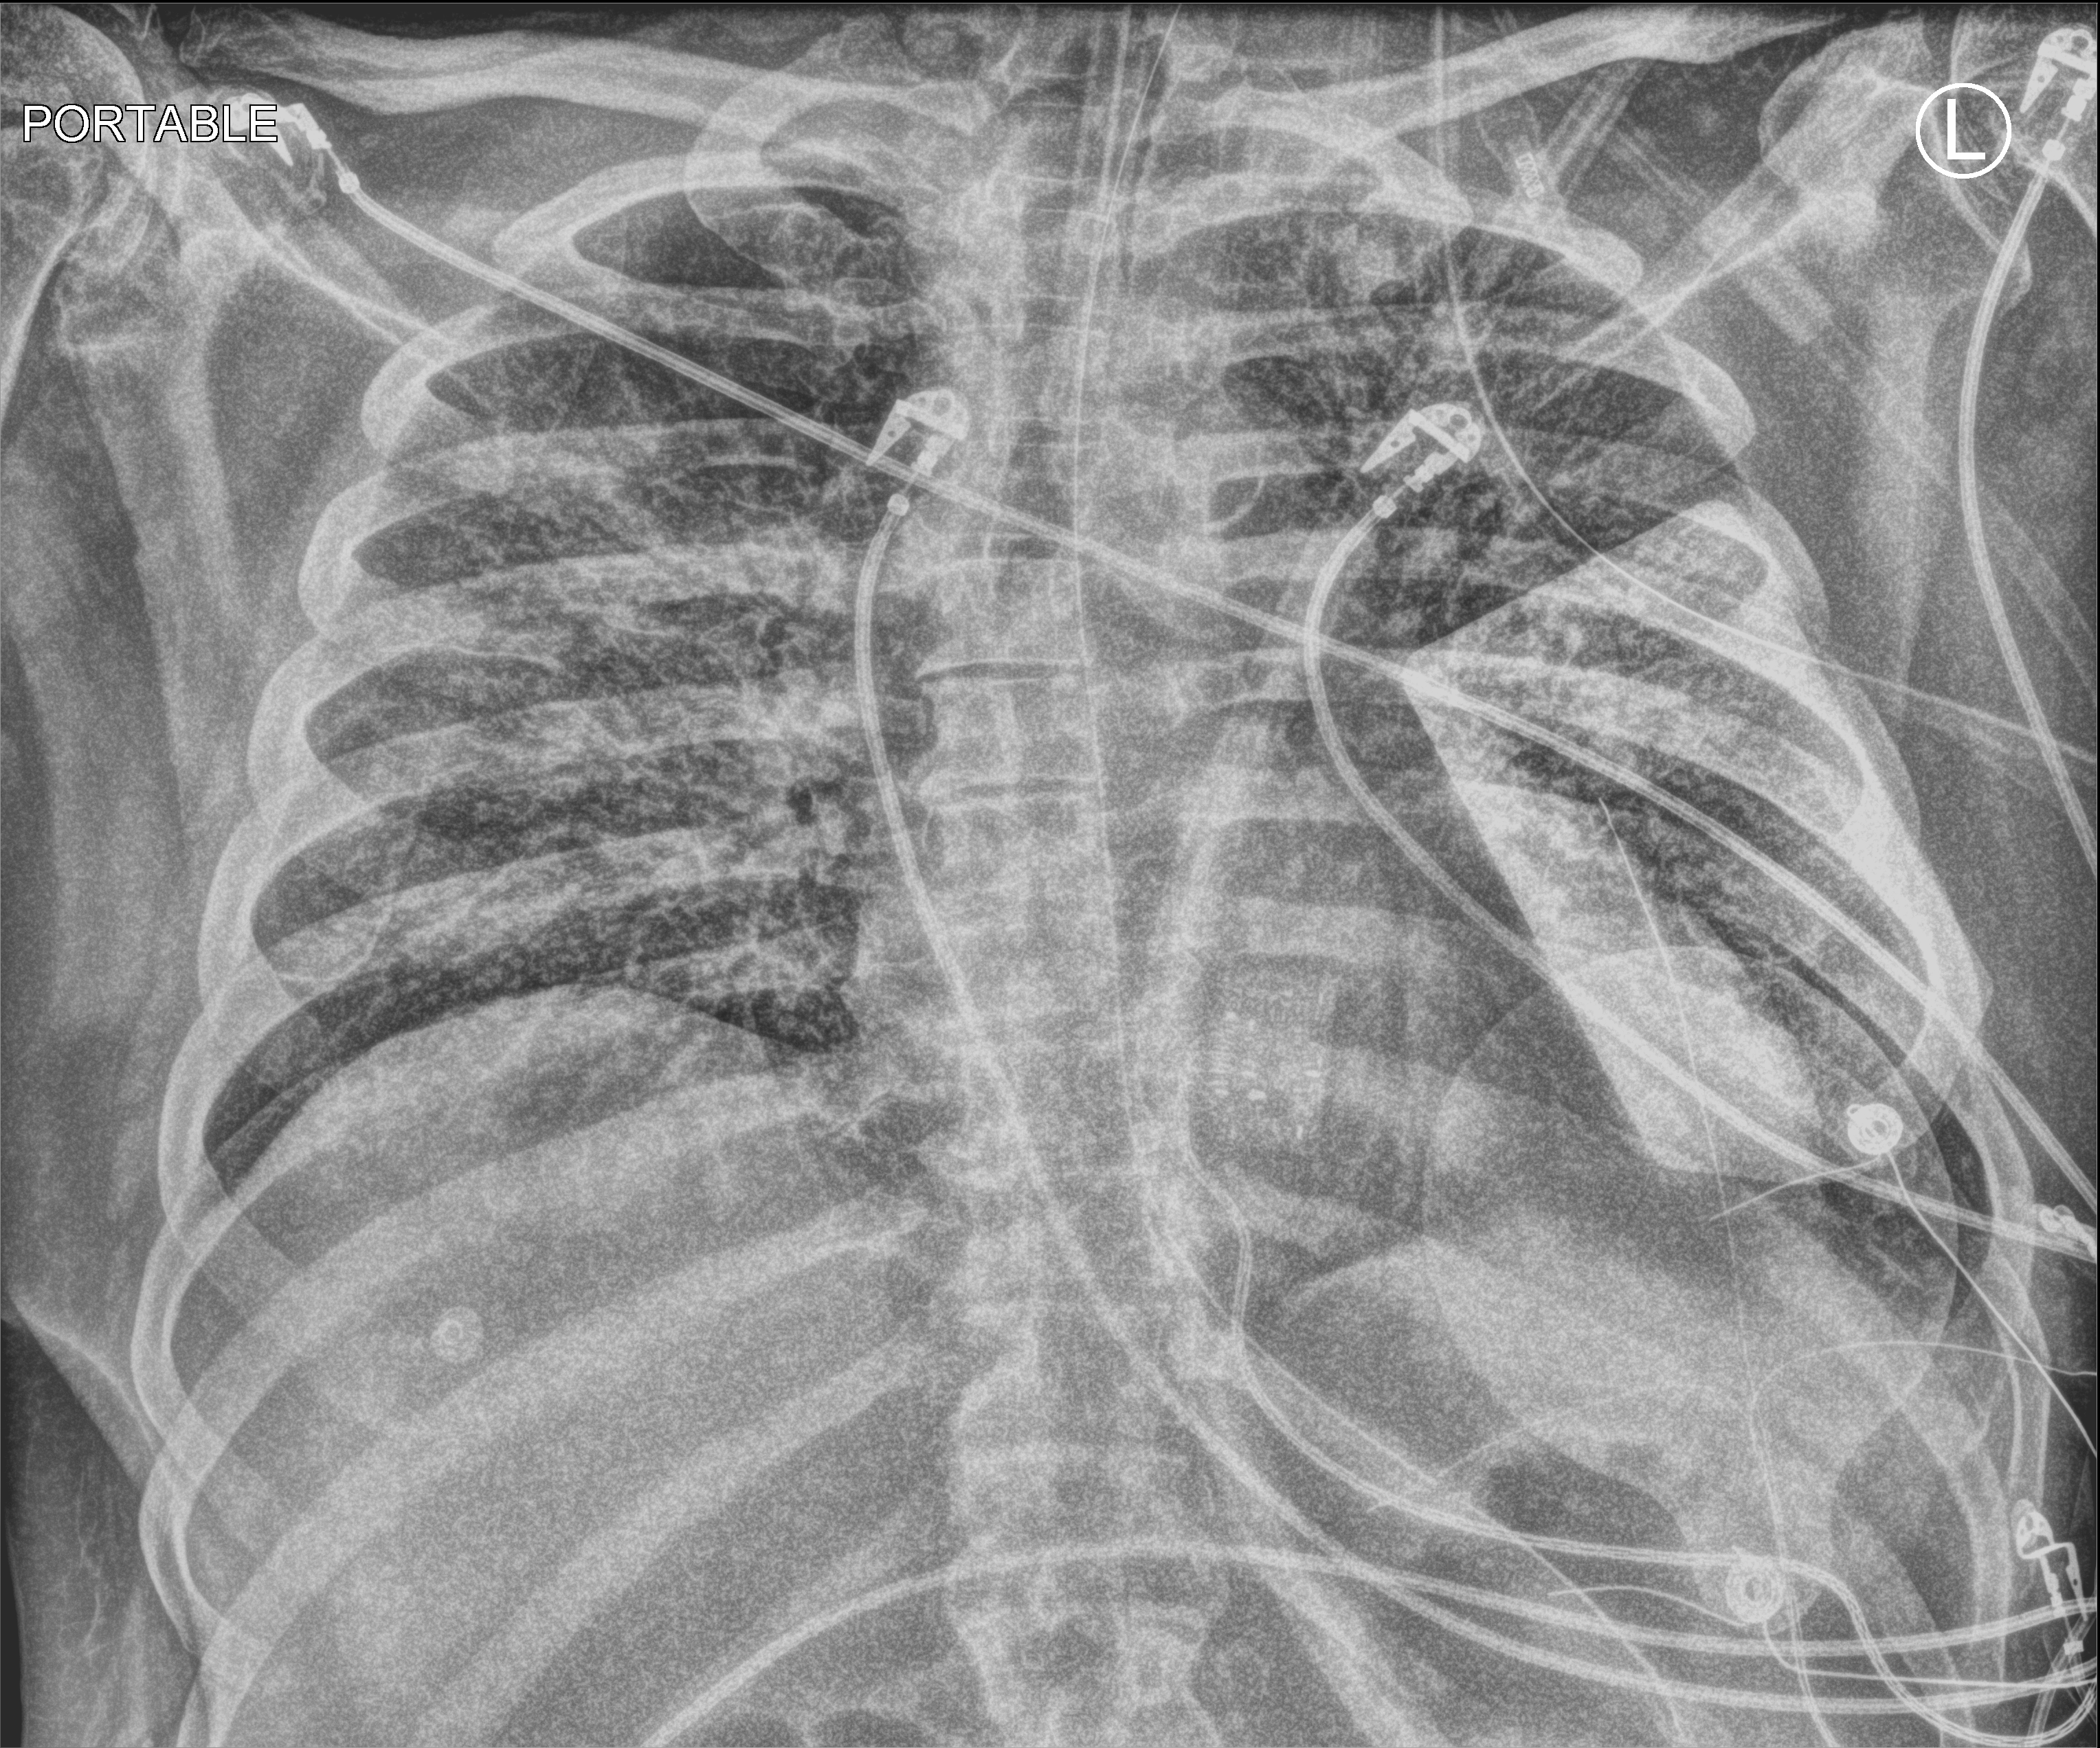
Bedside chest radiograph (computed radiography), anteroposterior (AP) projection. Male patient hospitalised with COVID-19, age 60–74 years.
Admission-level facts for this patient (not findings on this image; timing relative to this image not recorded): COPD (admission record): no; admitted to intensive care during this hospital stay: yes; other chronic lung disease (admission record): no.